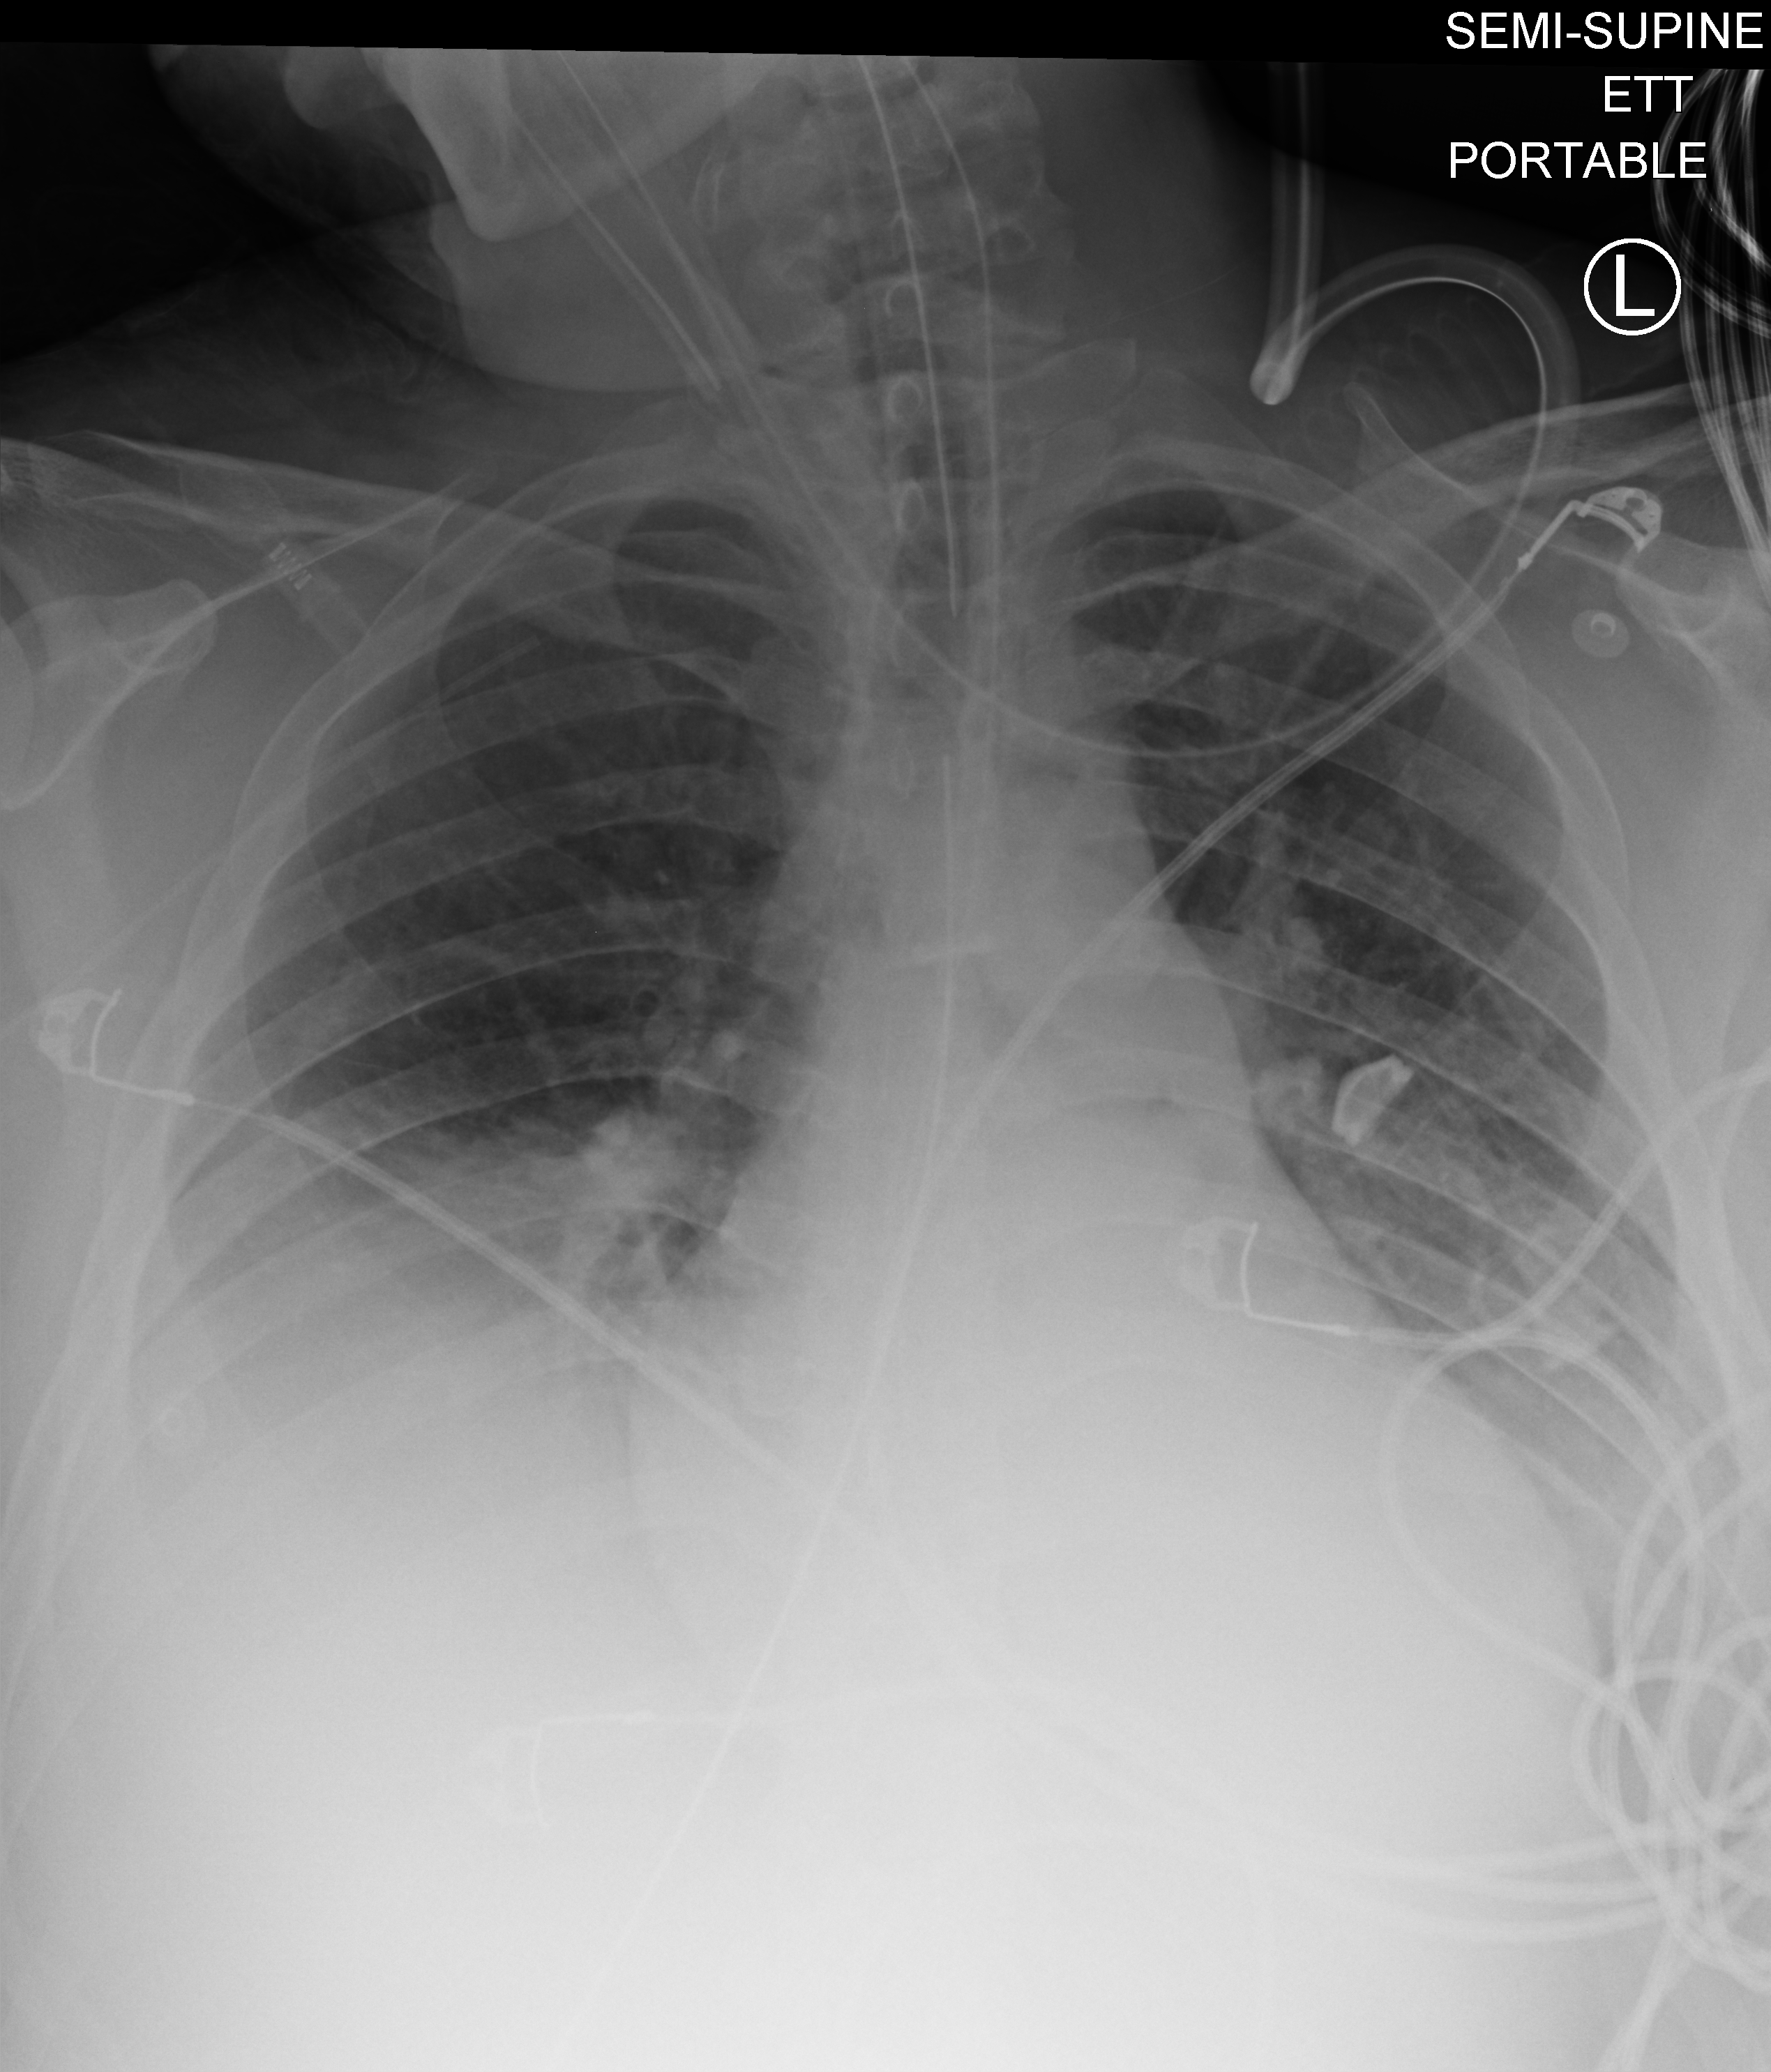
Bedside chest radiograph (computed radiography); anteroposterior (AP) projection. Male patient hospitalised with COVID-19, age 18–59 years.
From the hospital-stay record, not from the radiograph (when in the stay this image was taken is not recorded): length of hospital stay: 61 days.